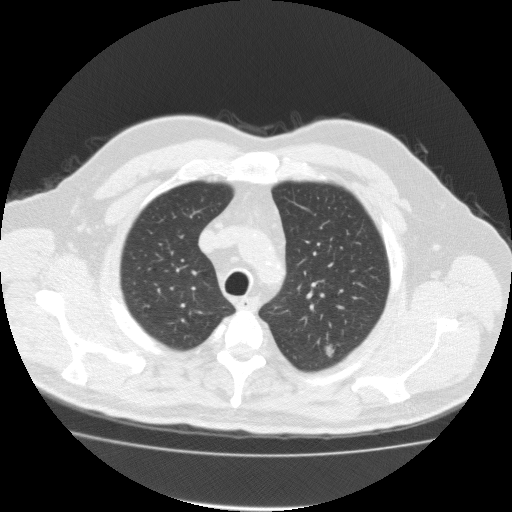
Axial slice from a low-dose chest CT screening exam. Baseline screening round. Lung window (W 1500 / L -600 HU). 2 mm slice thickness. Standard (soft-tissue) reconstruction kernel (FC10). Slice 28 of 161 in the series. 512 × 512 image matrix, field of view 412 × 412 mm. Male, age 57 years at enrolment.
Lesion marked by an expert reader, bounding box [x1, y1, x2, y2] px = [318, 336, 351, 371]. The exam's reader record, not a measurement of the box and not confirmed to be the same lesion: non-calcified nodule or mass ≥4 mm, left upper lobe, 11 × 8 mm, spiculated (stellate) margins, soft tissue attenuation. Official screen result: positive, change unspecified: nodule(s) >= 4 mm or enlarging nodule(s), mass(es), or other non-specific abnormalities suspicious for lung cancer. Participant outcome: lung cancer diagnosed 19 days after this screen — bronchiolo-alveolar adenocarcinoma, NOS, left upper lobe, well differentiated (G1), stage IA (AJCC 6th edition), 80 mm at pathology.